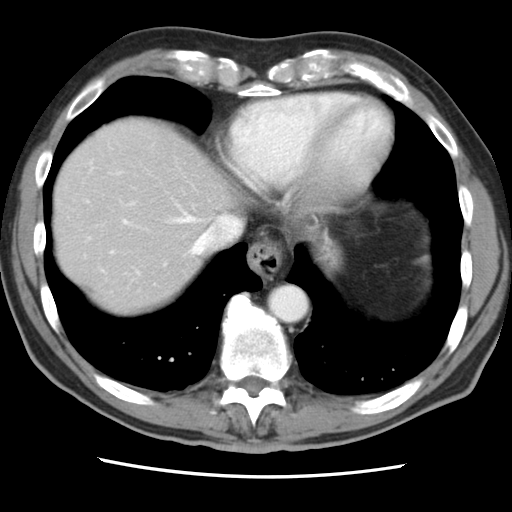
Contrast-enhanced abdominal CT, one axial slice. Slice 74 of 83 in the series (ordered by position). Intravenous contrast given. Soft-tissue window (W 400 / L 40 HU). 5 mm slice thickness. 512 × 512 image matrix, field of view 321 × 321 mm. Male patient, age 69 years. From the clinical record (not read from this slice): diagnosis: colorectal cancer liver metastases, imaged before liver resection; multiple liver metastases: yes; largest metastasis: 3.5 cm; disease in both lobes: no.
Structures marked on this image (expert manual segmentation):
- hepatic veins: bounding box <171,212,240,255> (left, top, right, bottom; pixels)
- liver: <54,117,233,316>
- planned liver remnant (the part of the liver to remain after resection): <54,153,212,316>
- portal vein (with intrahepatic branches): <122,219,129,224>